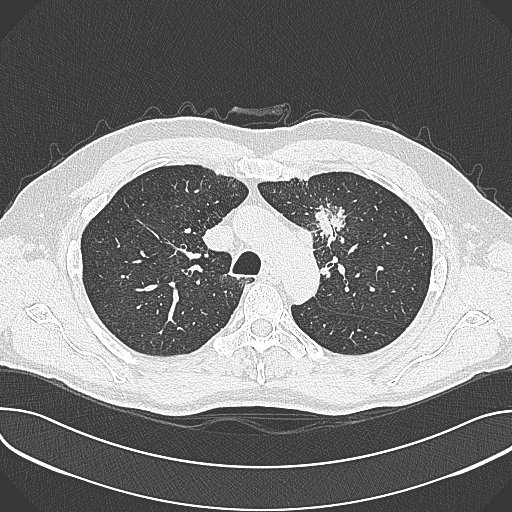
Chest CT (low-dose screening protocol), one axial image; first (baseline) screen; lung window (W 1500 / L -600 HU); 1 mm slice thickness; lung (sharp) reconstruction kernel (B80f); 512 × 512 image matrix, field of view 380 × 380 mm. Male, age 59 years at enrolment. Current smoker at enrolment.
Expert-annotated lung lesion, bounding box <302,199,359,257> (left, top, right, bottom; pixels). The screening reader recorded 2 non-calcified nodules or masses ≥4 mm on this exam (left upper lobe, left upper lobe); which of them this box marks is not recorded. Official screen result: positive, change unspecified: nodule(s) >= 4 mm or enlarging nodule(s), mass(es), or other non-specific abnormalities suspicious for lung cancer. Participant outcome: lung cancer diagnosed 21 days after this screen — non-small cell carcinoma, left upper lobe, poorly differentiated (G3), stage IIIA (AJCC 6th edition), 35 mm at pathology.